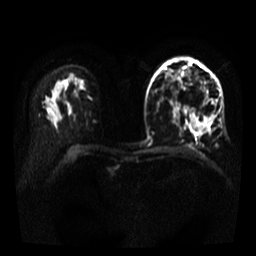
Breast MRI, one axial slice. Slice 22 of 35 in the series (ordered by position). Diffusion-weighted series; image 2 of 4 stored at this slice position (different b-values; order by instance number). 3 T. 5 mm slice thickness. 256 × 256 image matrix, field of view 320 × 320 mm. Female patient.
Outlined on this slice (expert manual segmentation):
- tumour on diffusion-weighted imaging: bounding box (x1, y1, x2, y2) in pixels: (192, 111, 212, 132)